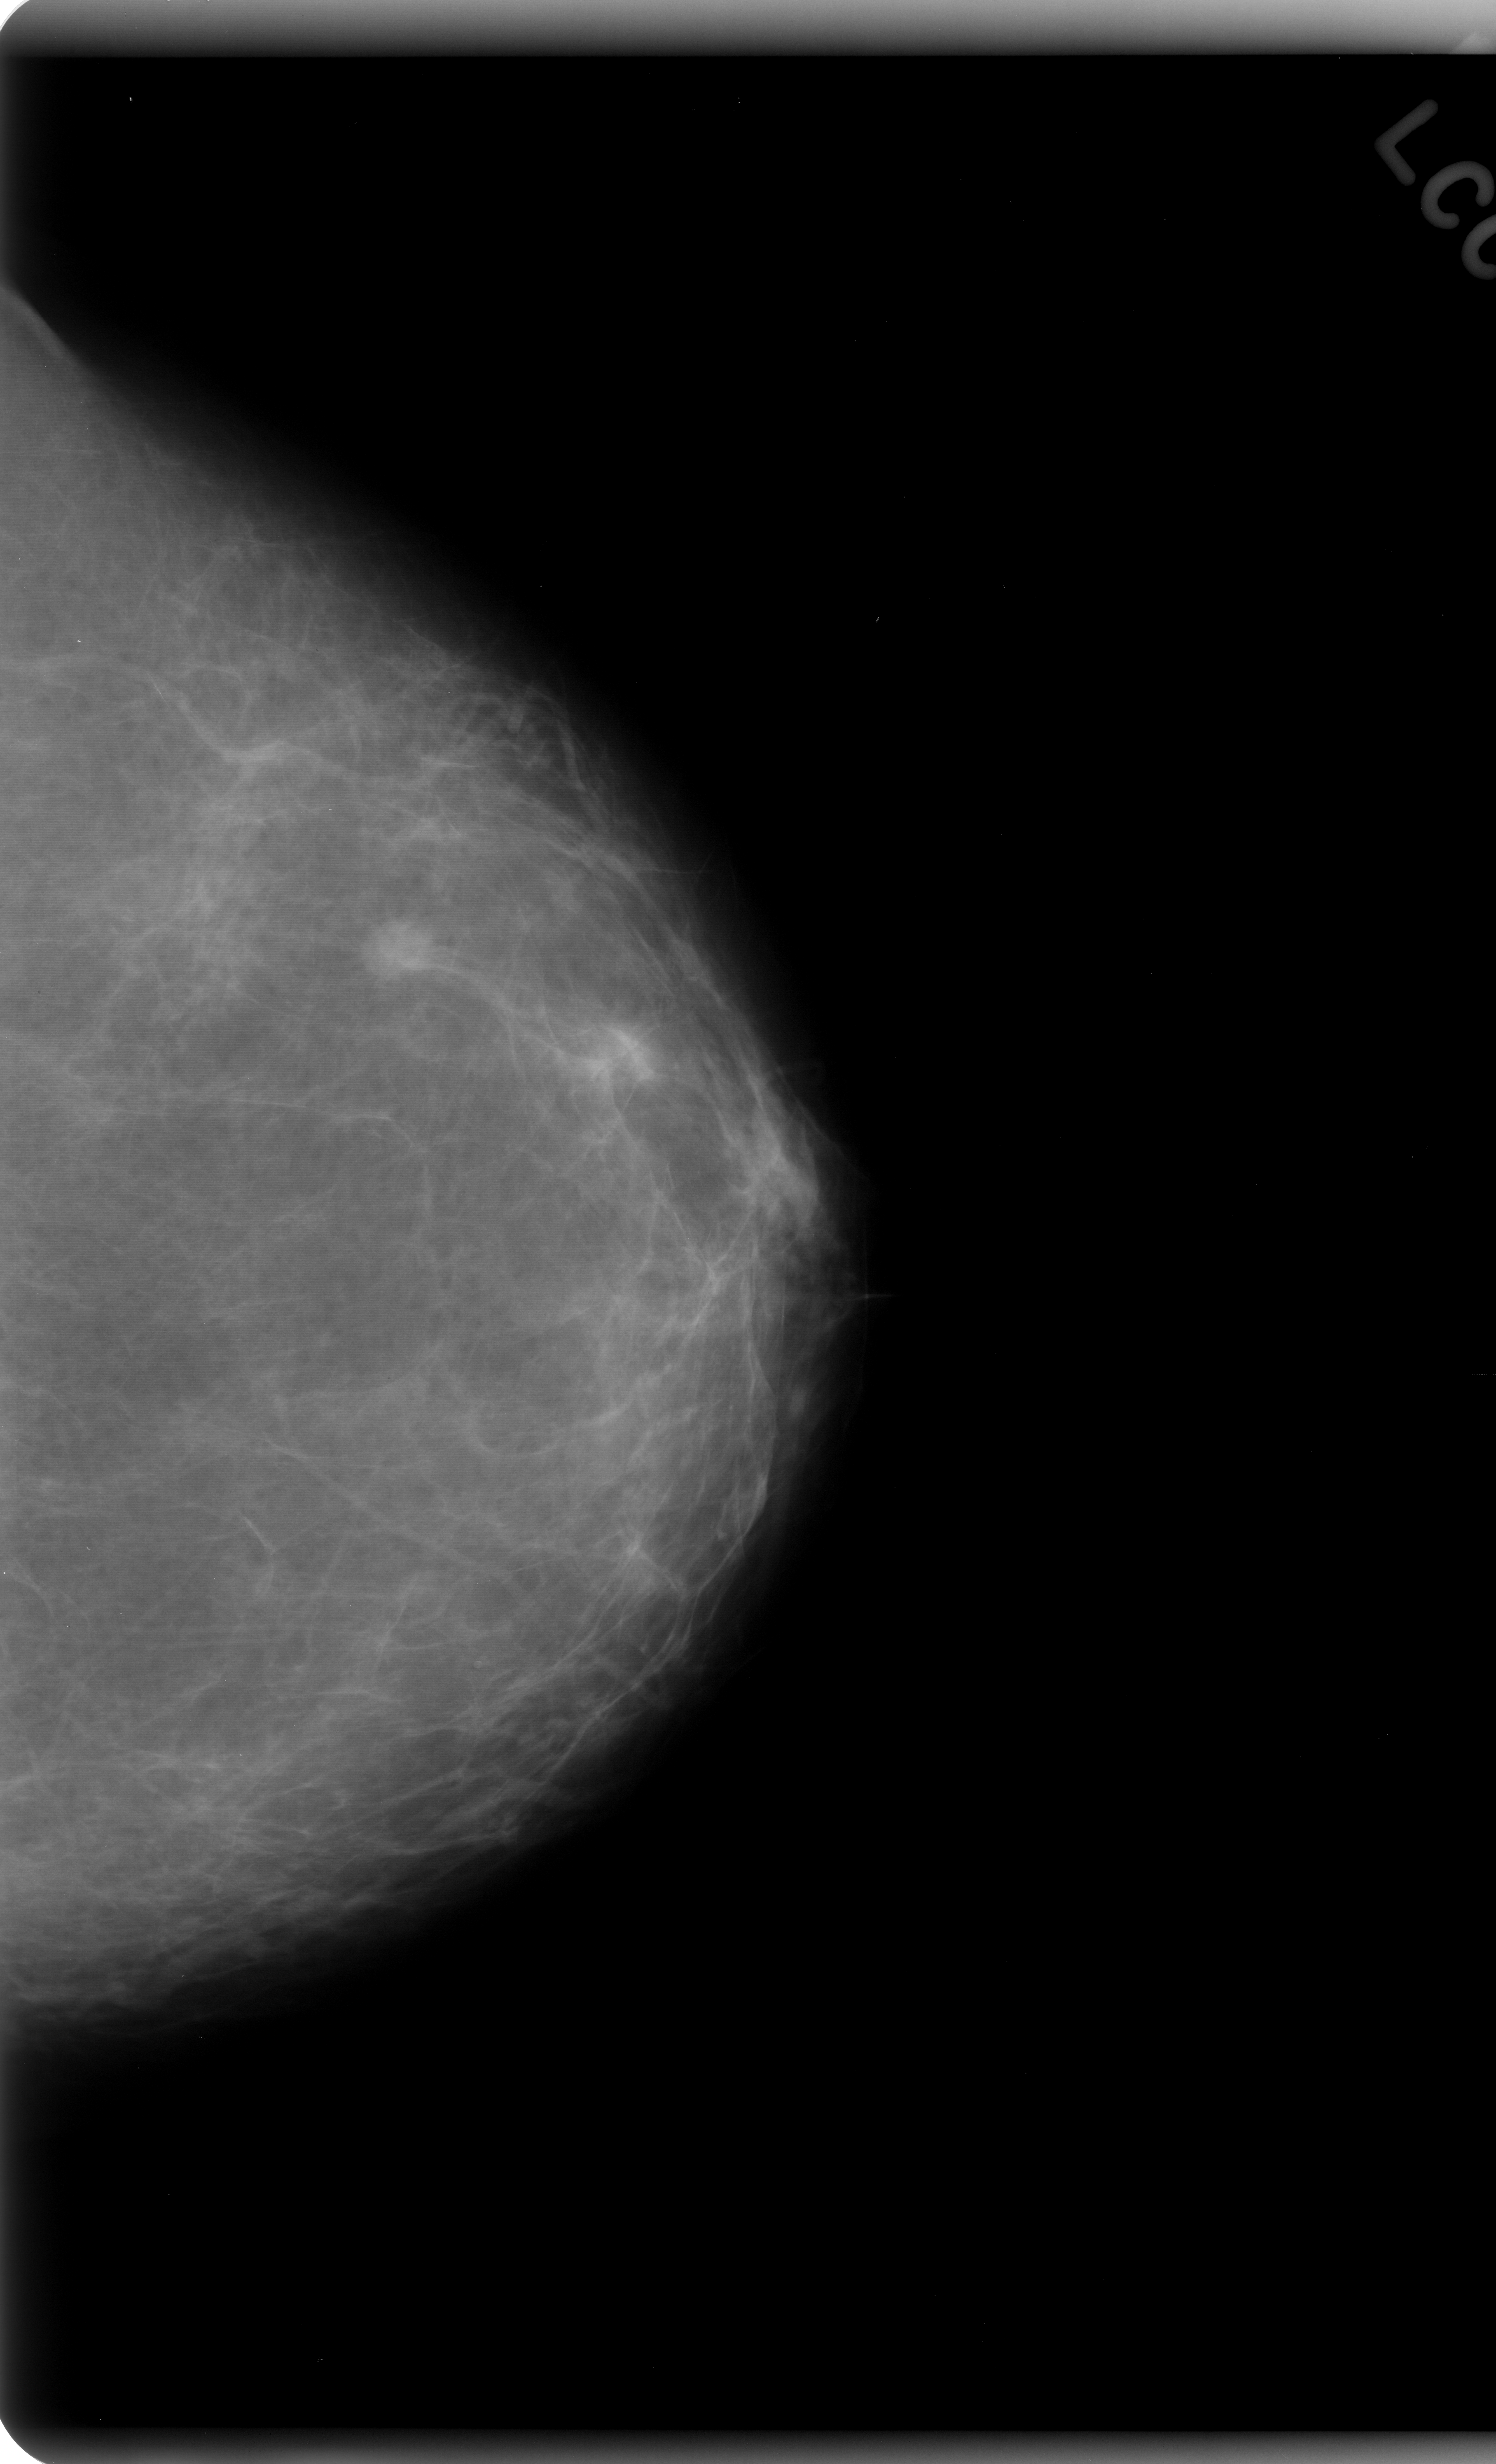
Digitized screen-film mammogram; left breast; craniocaudal (CC) view; BI-RADS breast density category 1 (scale 1–4).
Marked findings (only marked abnormalities are described; nothing is implied about the rest of the image): mass, shape round, margins spiculated; BI-RADS assessment category 5; subtlety rating 5 on a 1 (subtle) to 5 (obvious) scale; pathology result (as recorded, not read from the image): malignant.